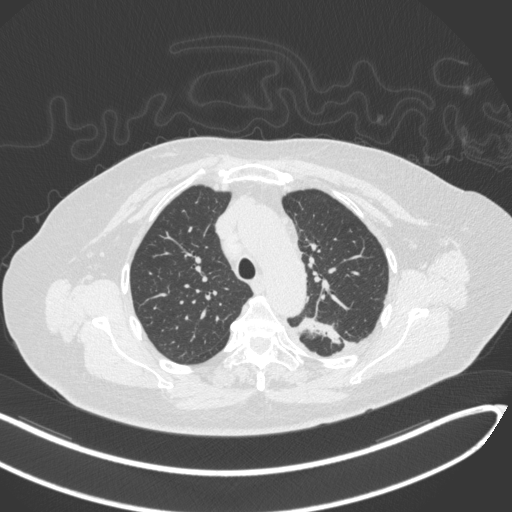
Chest CT, one axial slice. 120 kVp. Lung window (W 1500 / L -600 HU). 512 × 512 image matrix, field of view 400 × 400 mm. Patient: female, 76 years. From the clinical record (not read from this slice): clinical TNM (as recorded): T1c N0 M0.
Structures marked on this image (rectangle marked by the reading radiologist):
- lung tumour (recorded histology: adenocarcinoma): box from (x=293, y=311) to (x=344, y=348) px